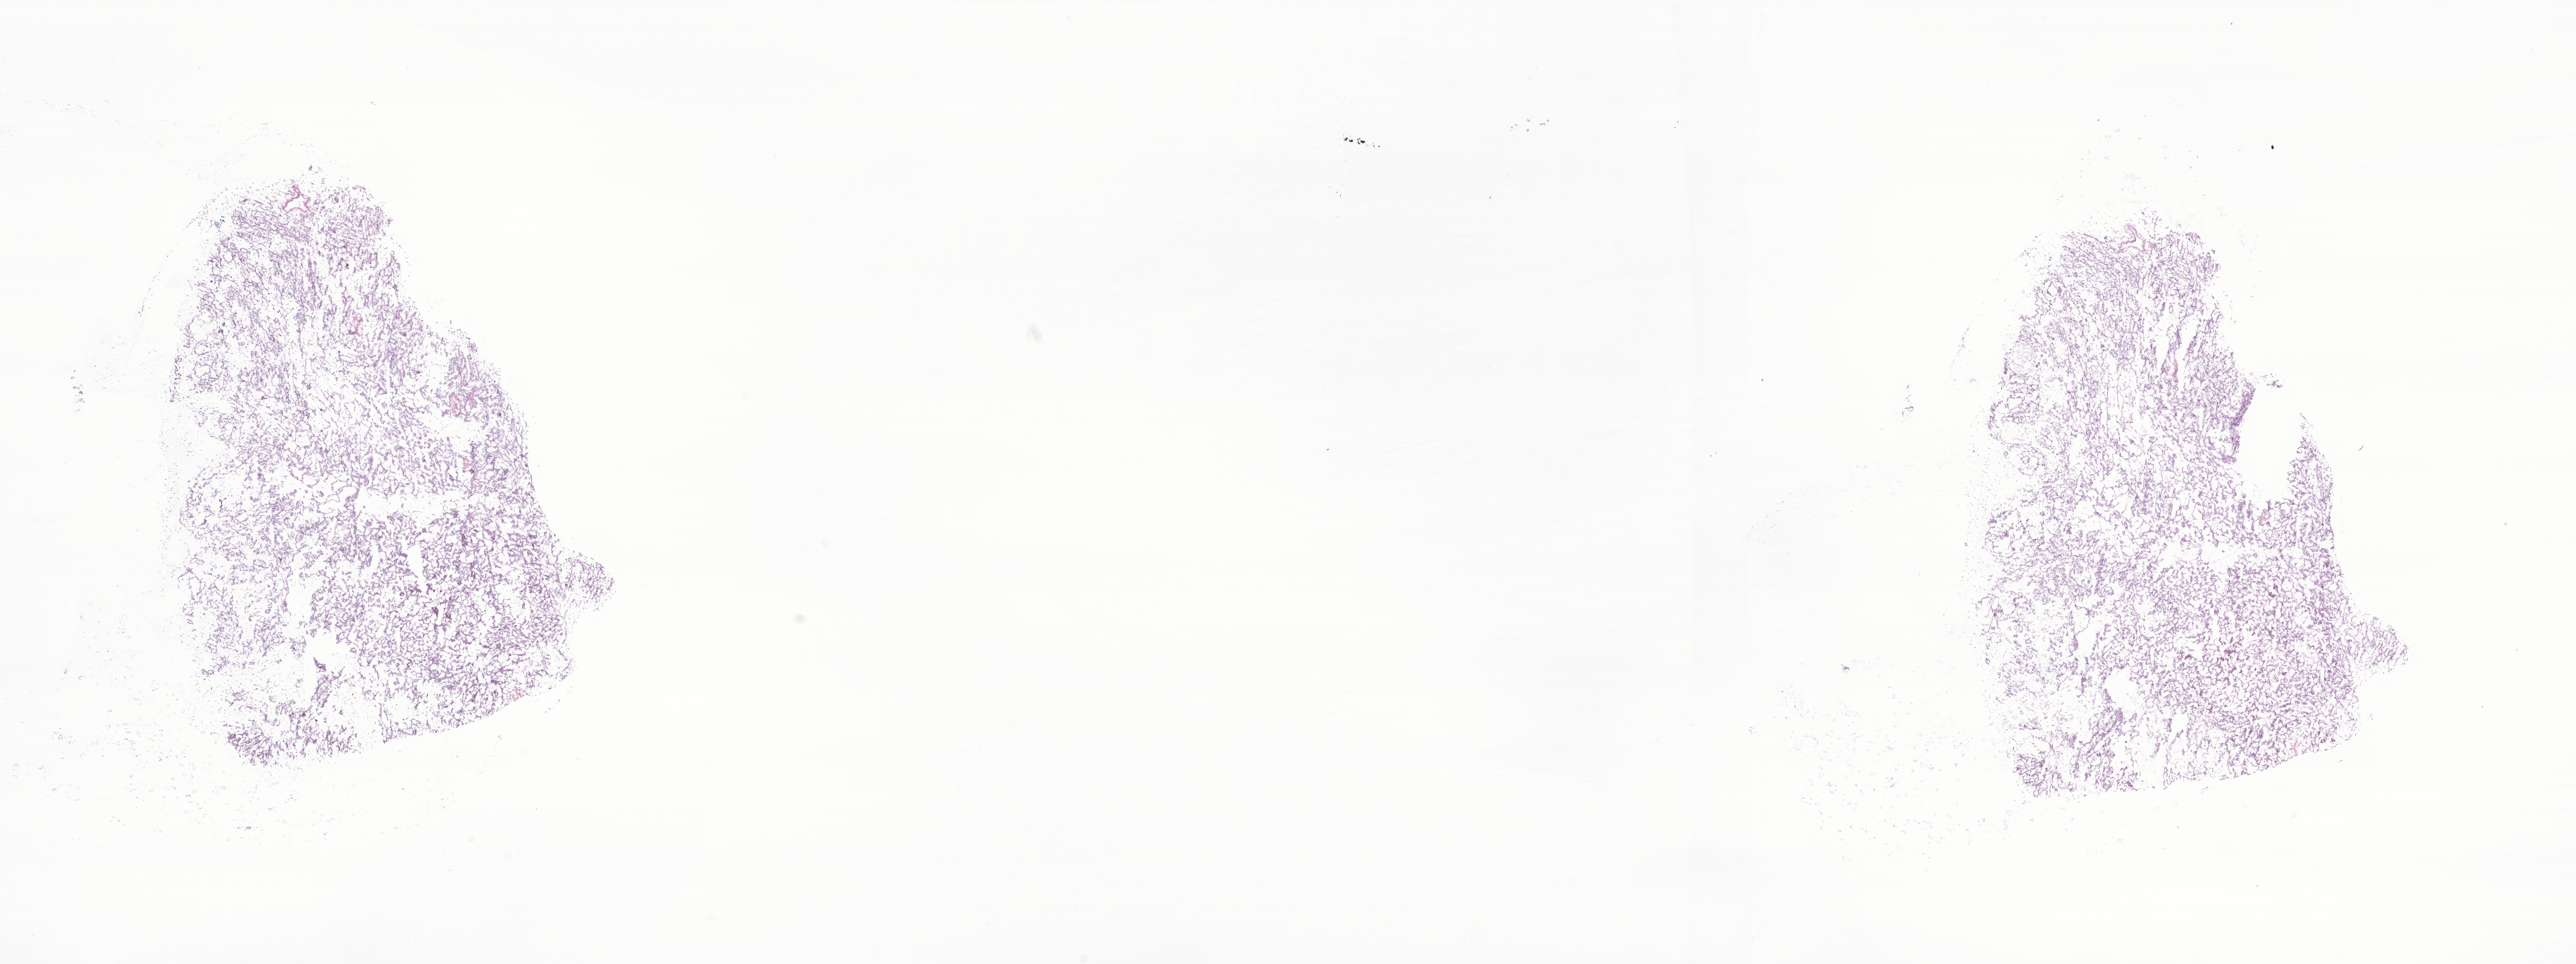
Whole-slide image, H&E stain of tumor tissue from the cerebral ventricle, shown as a low-resolution overview of the whole scanned area (about 28.0 x 10.5 mm). Frozen section. Patient male; age 89 months.
* diagnosis: Choroid plexus carcinoma